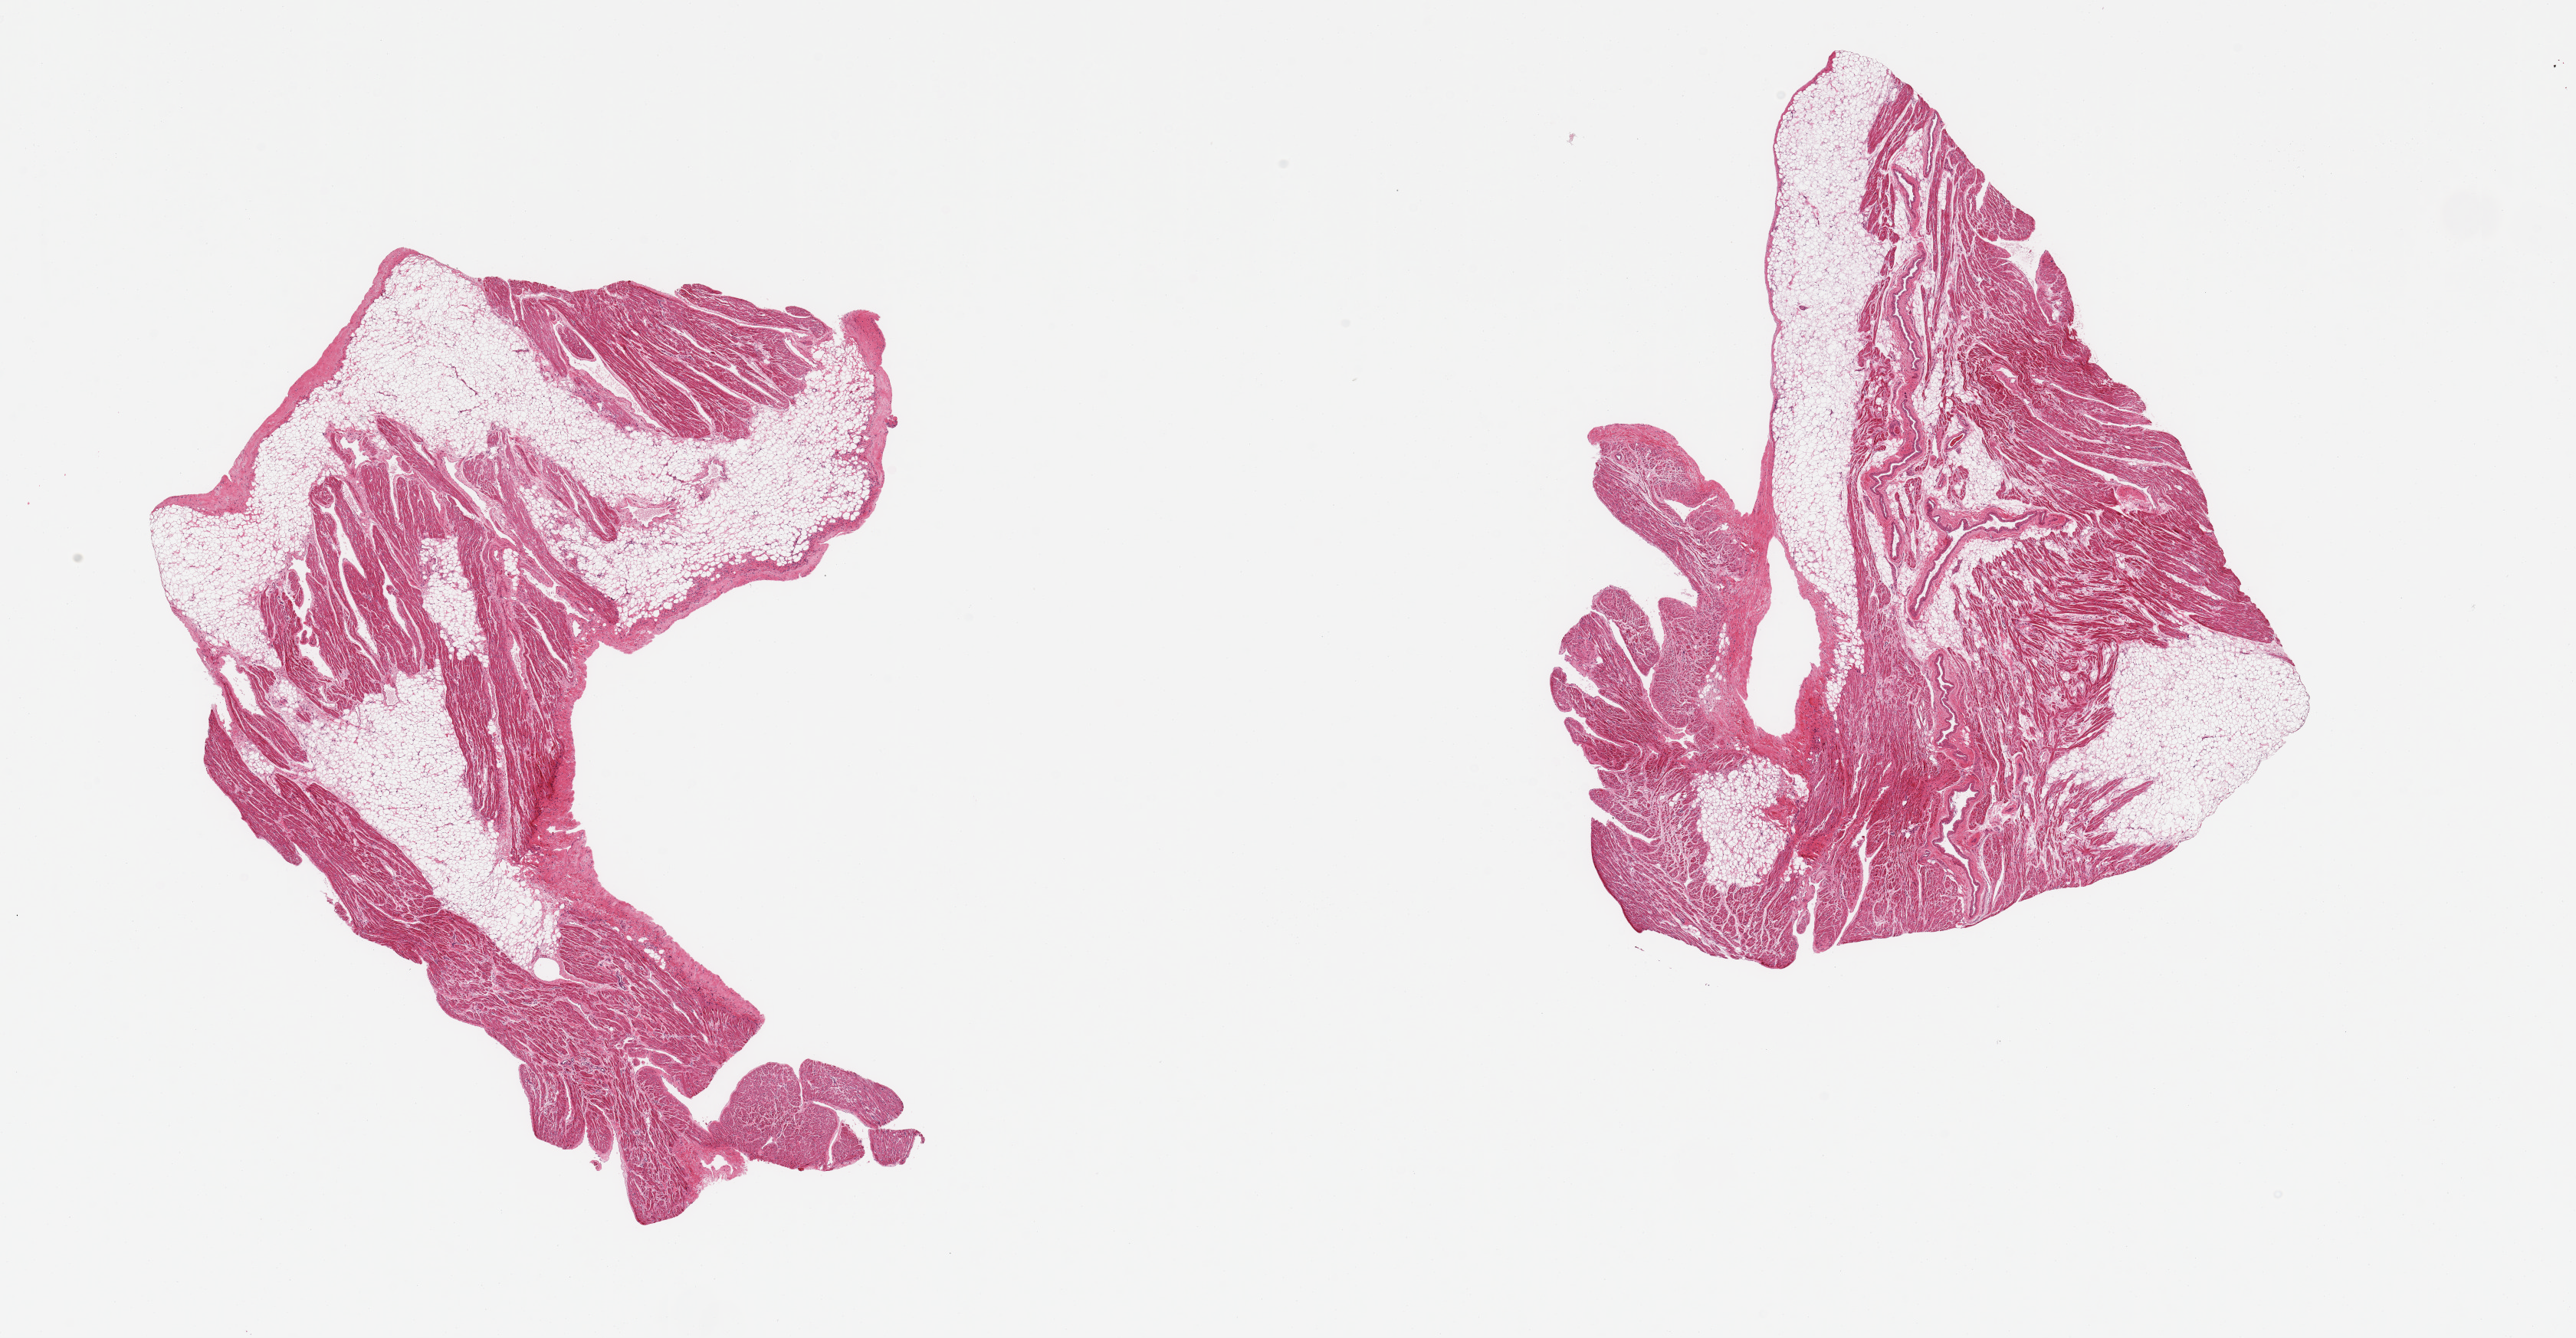
Whole-slide image, H&E stain, brightfield, low-resolution overview of the scanned area, about 26.6 x 13.8 mm. PAXgene-fixed, paraffin-embedded tissue. Sampled site (target tissue): auricular appendage. Tissue donor sample. Male donor.
* reviewer comment on this tissue sample: 2 pieces; ~50% and ~40% internal fat